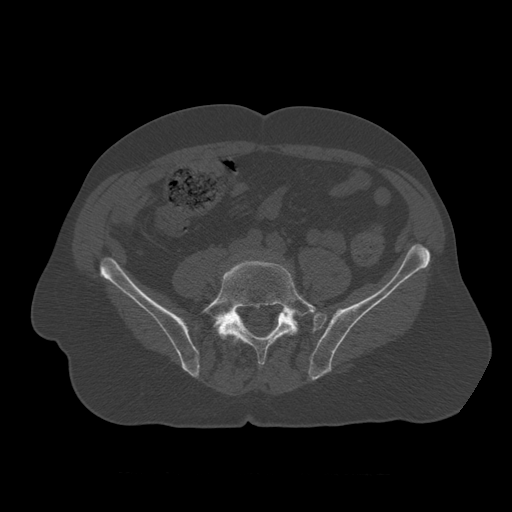
CT including the spine, one axial slice. Slice 256 of 450 in the series (ordered by position). Reconstruction kernel STANDARD. Bone window (W 1800 / L 400 HU). 1.25 mm slice thickness. 512 × 512 image matrix, field of view 405 × 405 mm. Patient age 75 years. Case-level facts recorded for this patient, not image findings: primary cancer: prostate.
Structures marked on this image (semi-automatically segmented with operator editing):
- L4 vertebra: box from (x=232, y=322) to (x=234, y=325) px
- L5 vertebra: (x=202, y=260)–(x=317, y=368)